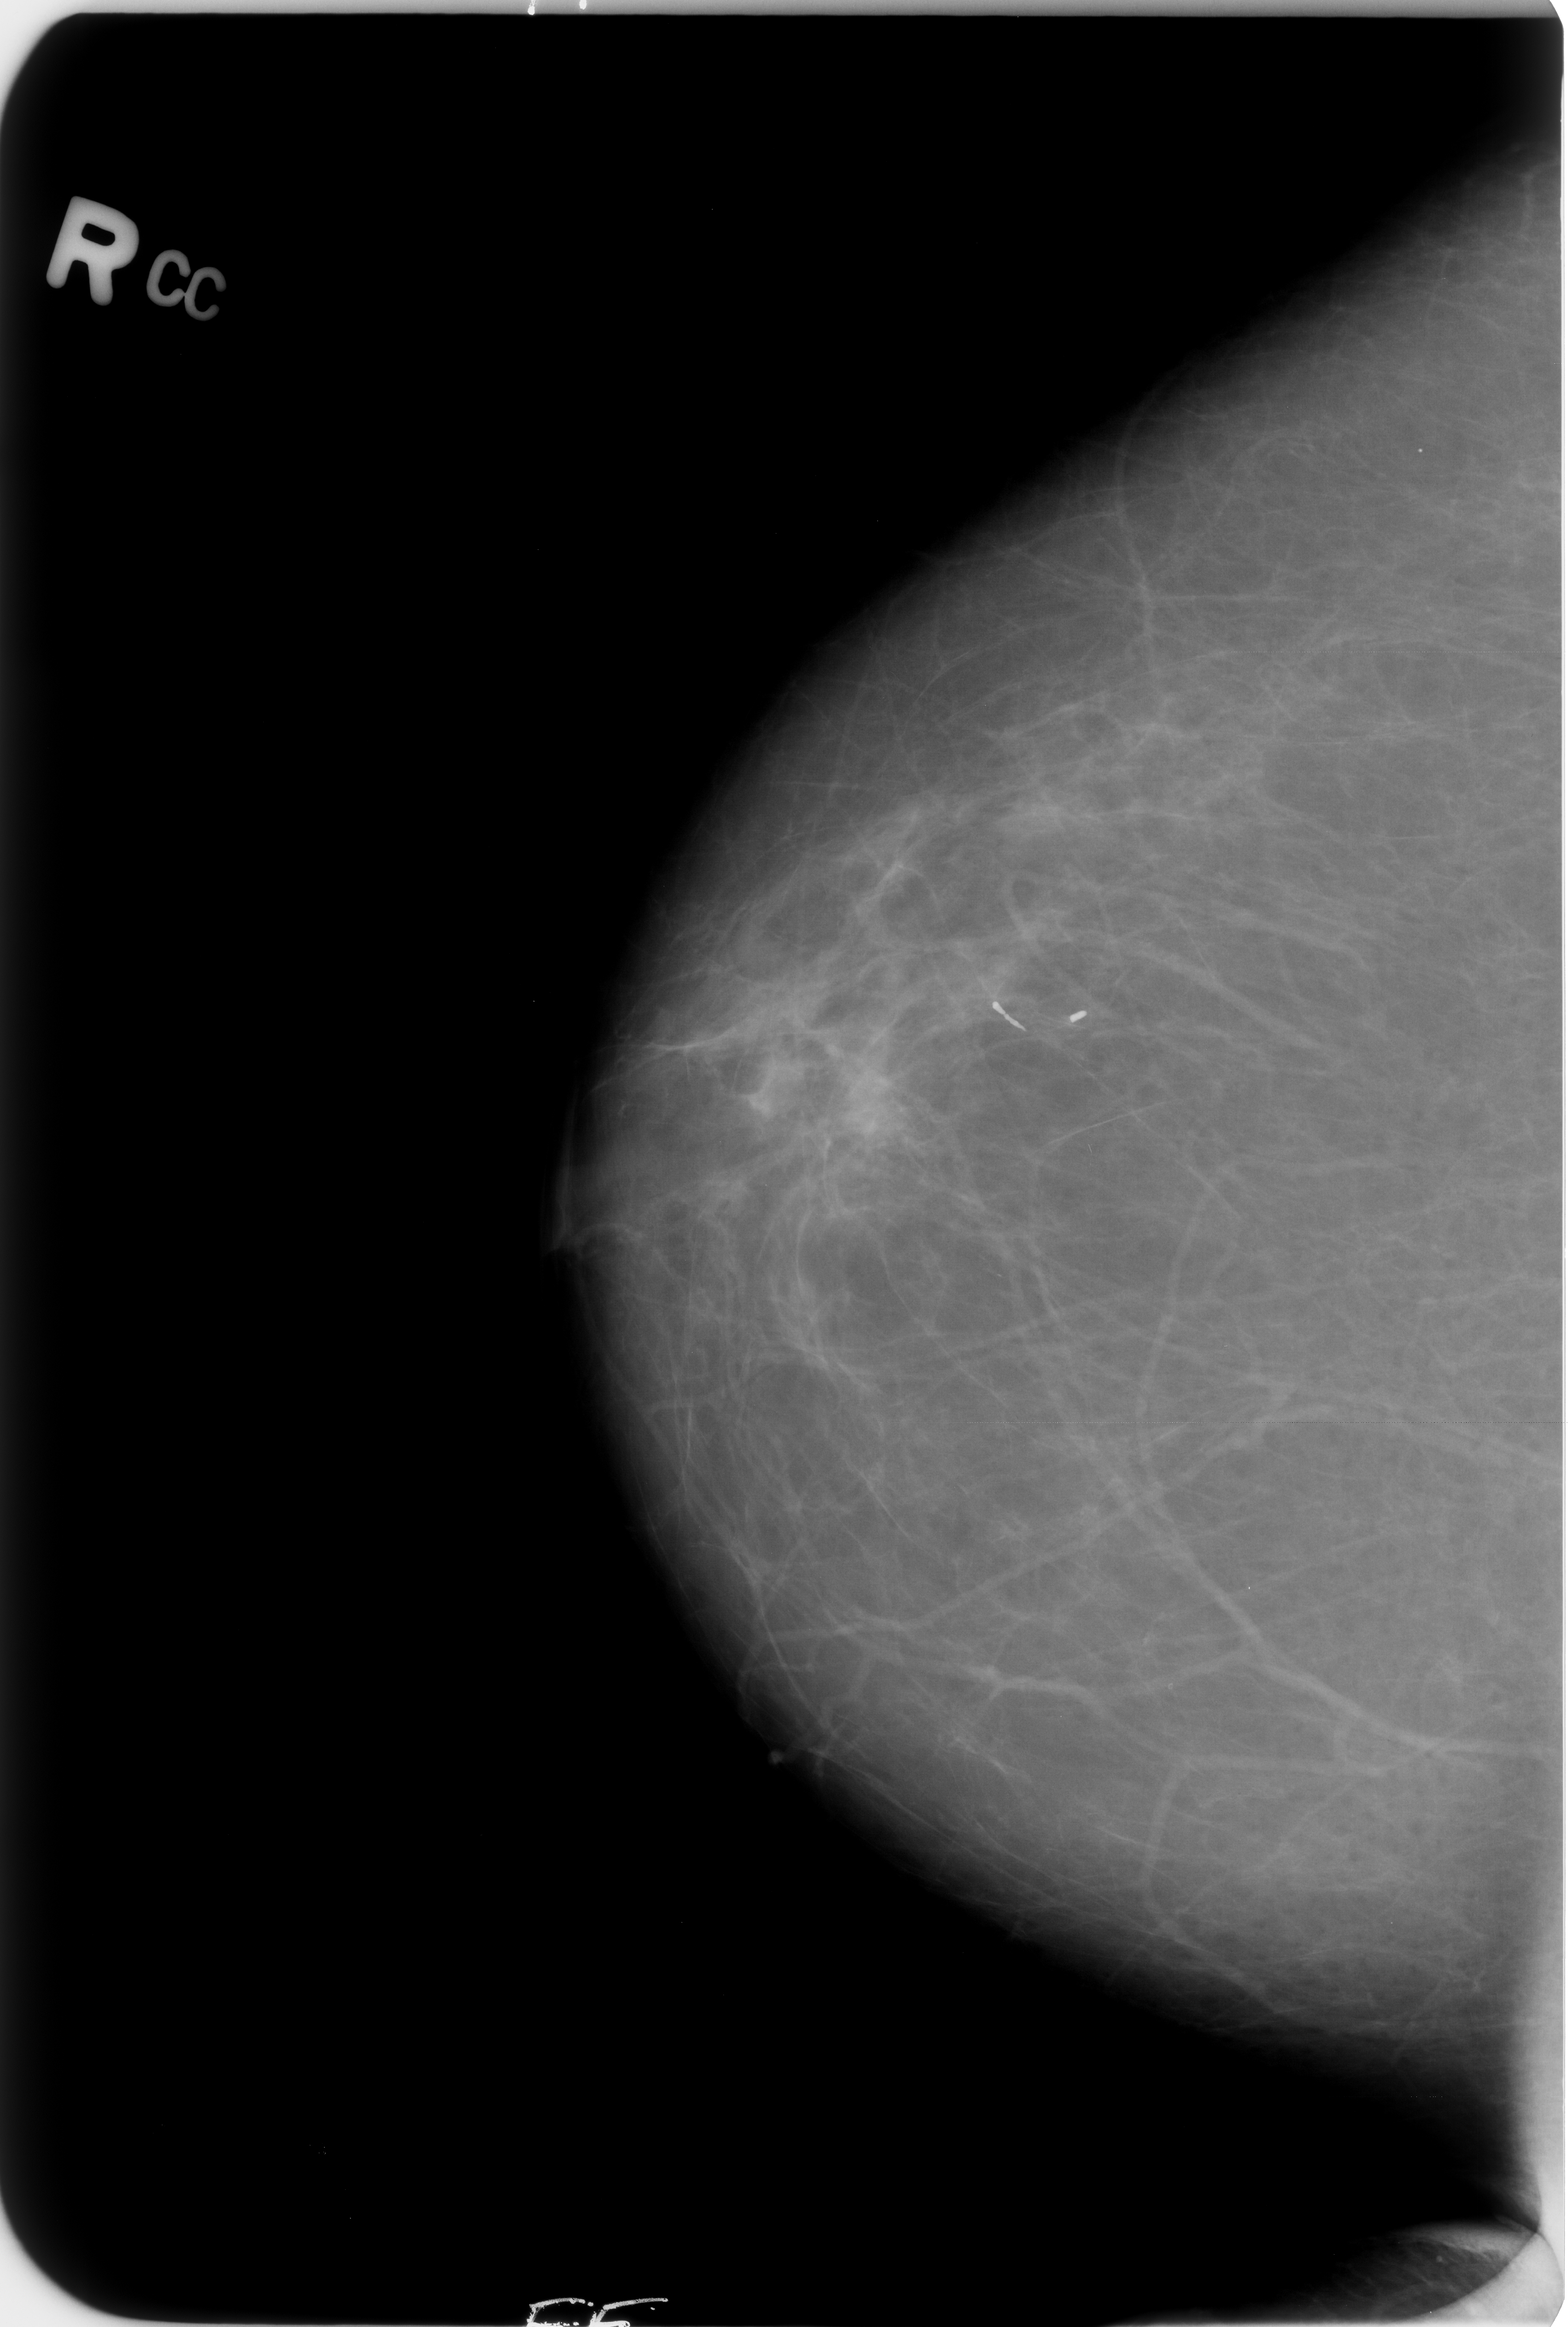
Digitized screen-film mammogram, right breast, CC view, BI-RADS breast density category 1 (scale 1–4).
Marked findings (only marked abnormalities are described; nothing is implied about the rest of the image): Finding 1 of 2: calcifications, morphology large rodlike, distribution segmental; BI-RADS assessment category 2; benign without callback (not worked up further). Finding 2 of 2: calcifications, morphology large rodlike, distribution segmental; BI-RADS assessment category 2; benign; no additional work-up was recommended (benign without callback).